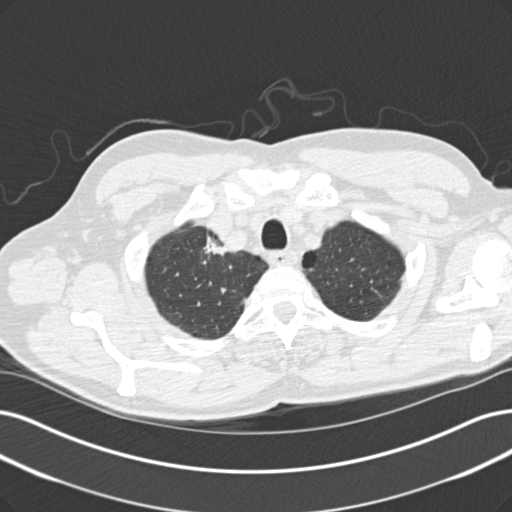
Low-dose screening chest CT, one axial slice. Slice 130 of 152 in the series (ordered by position). Lung window (W 1500 / L -600 HU). 2 mm slice thickness. 512 × 512 image matrix, field of view 365 × 365 mm.
Structures marked on this image (manually delineated by an expert):
- lesion 1 (tumor, upper lobe of right lung): bounding box <204,236,227,256> (left, top, right, bottom; pixels)